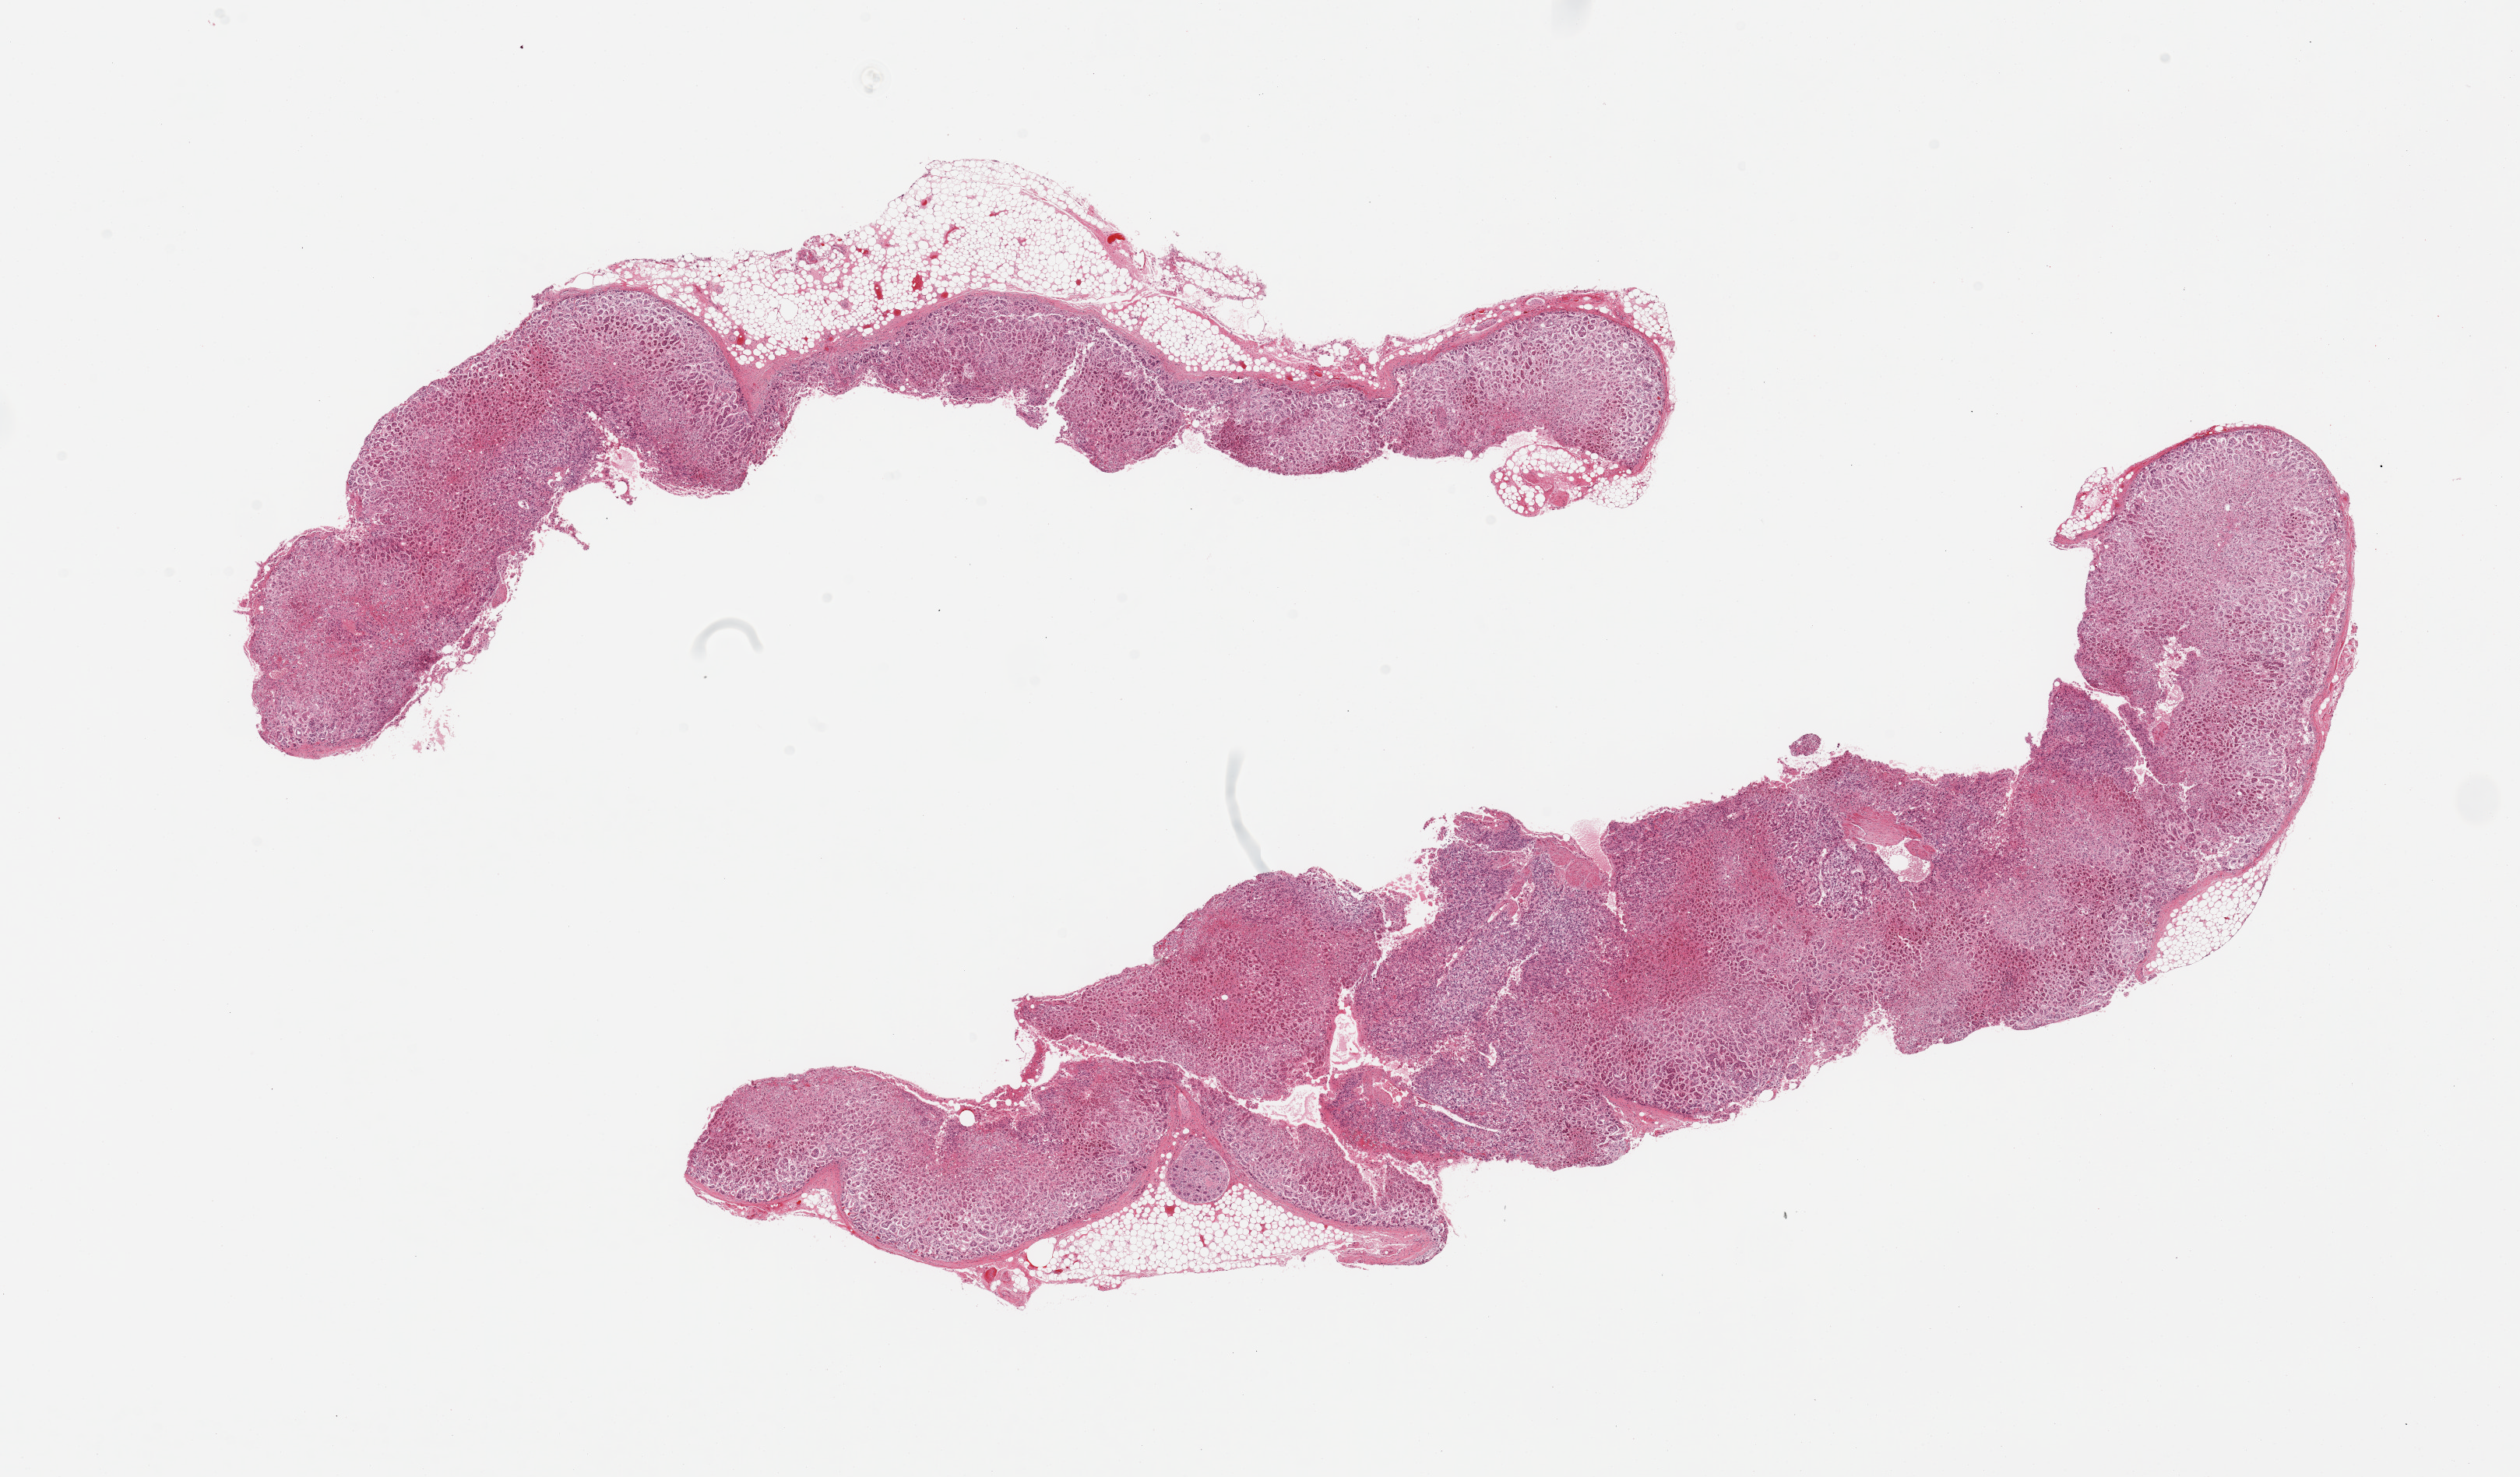
Haematoxylin and eosin whole-slide image, shown as a low-resolution overview of the whole scanned area (about 25.6 x 15.0 mm, from a 20x scan), PAXgene-fixed, paraffin-embedded tissue, target tissue: adrenal gland, donor tissue sample. Male donor.
Review note (as recorded): 2 pieces. external fat 30 and 10%.